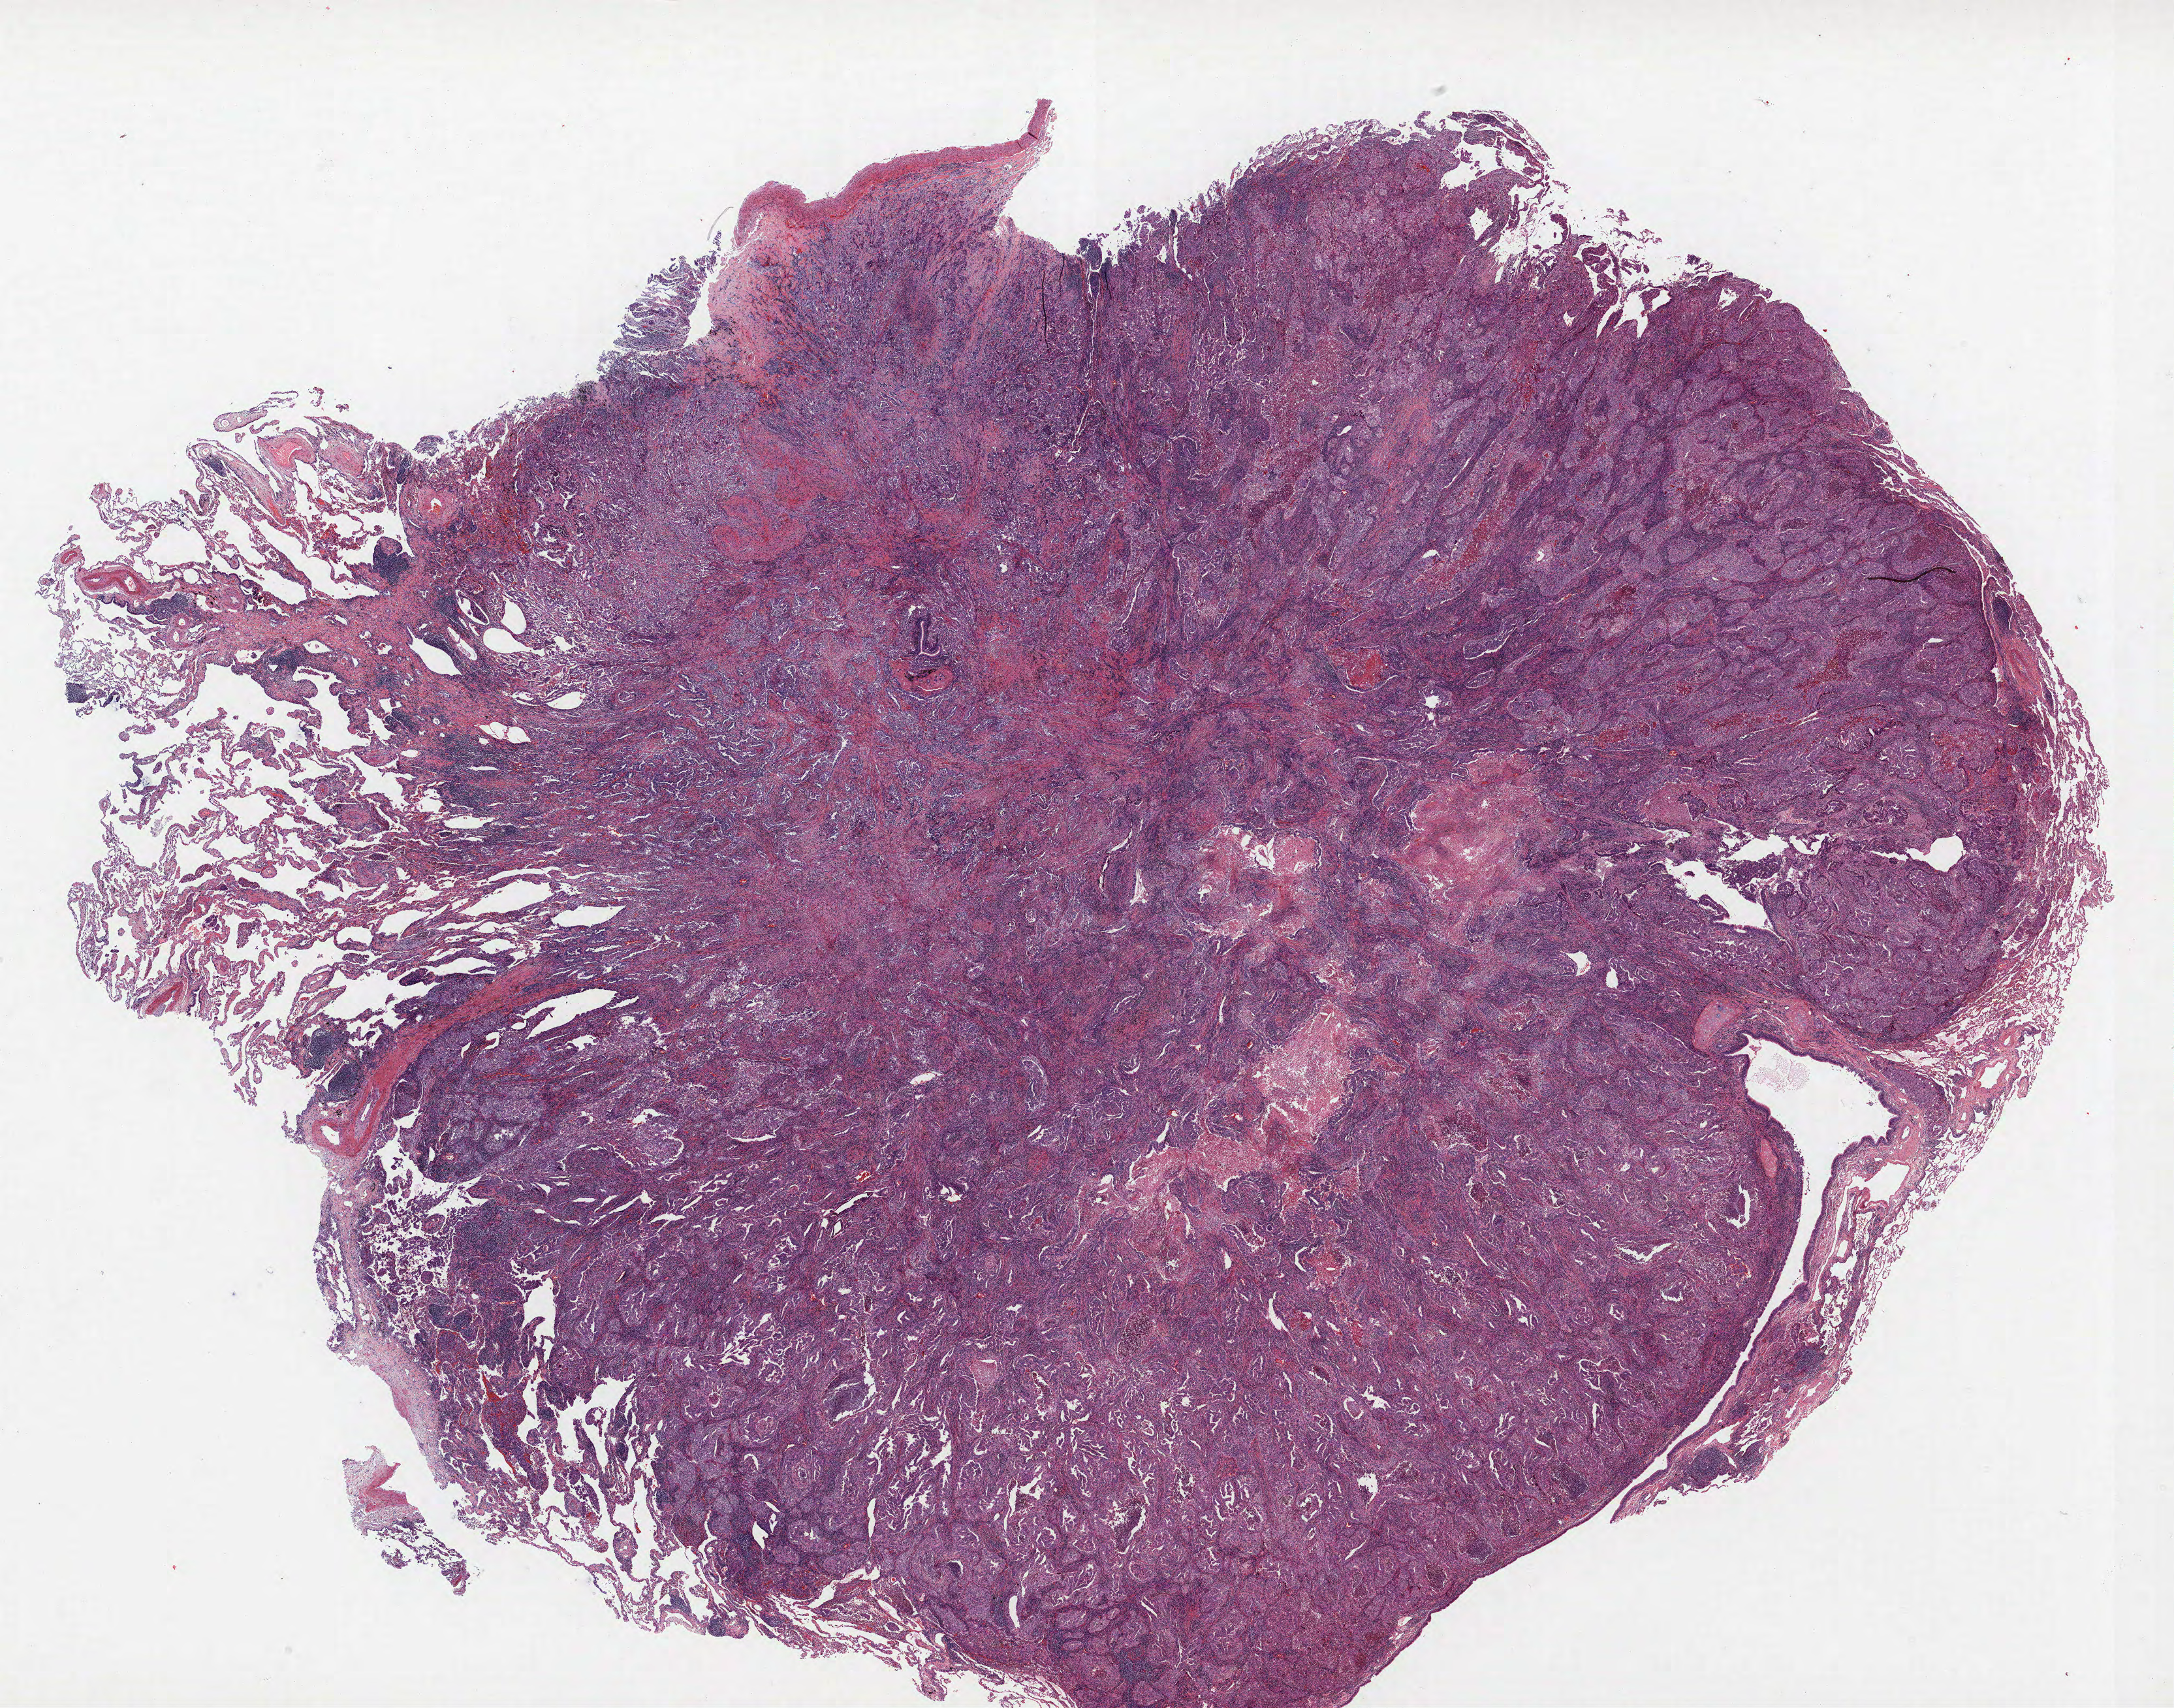
Hematoxylin and eosin (H&E) stained whole-slide image — shown as a low-resolution overview of the whole scanned area (about 26.6 x 20.9 mm); FFPE section; lung. Male patient, aged 59 at enrolment. Current smoker at enrolment. Grade: poorly differentiated (G3).
- tumour size (pathology): 34 mm
- participant's lung-cancer diagnosis: Large cell carcinoma, NOS (ICD-O-3 8012/3)
- ICD-O-3 topography: upper lobe of lung (C34.1)
- primary tumour location (clinical record): right upper lobe
- stage (AJCC 6th edition): IIIA